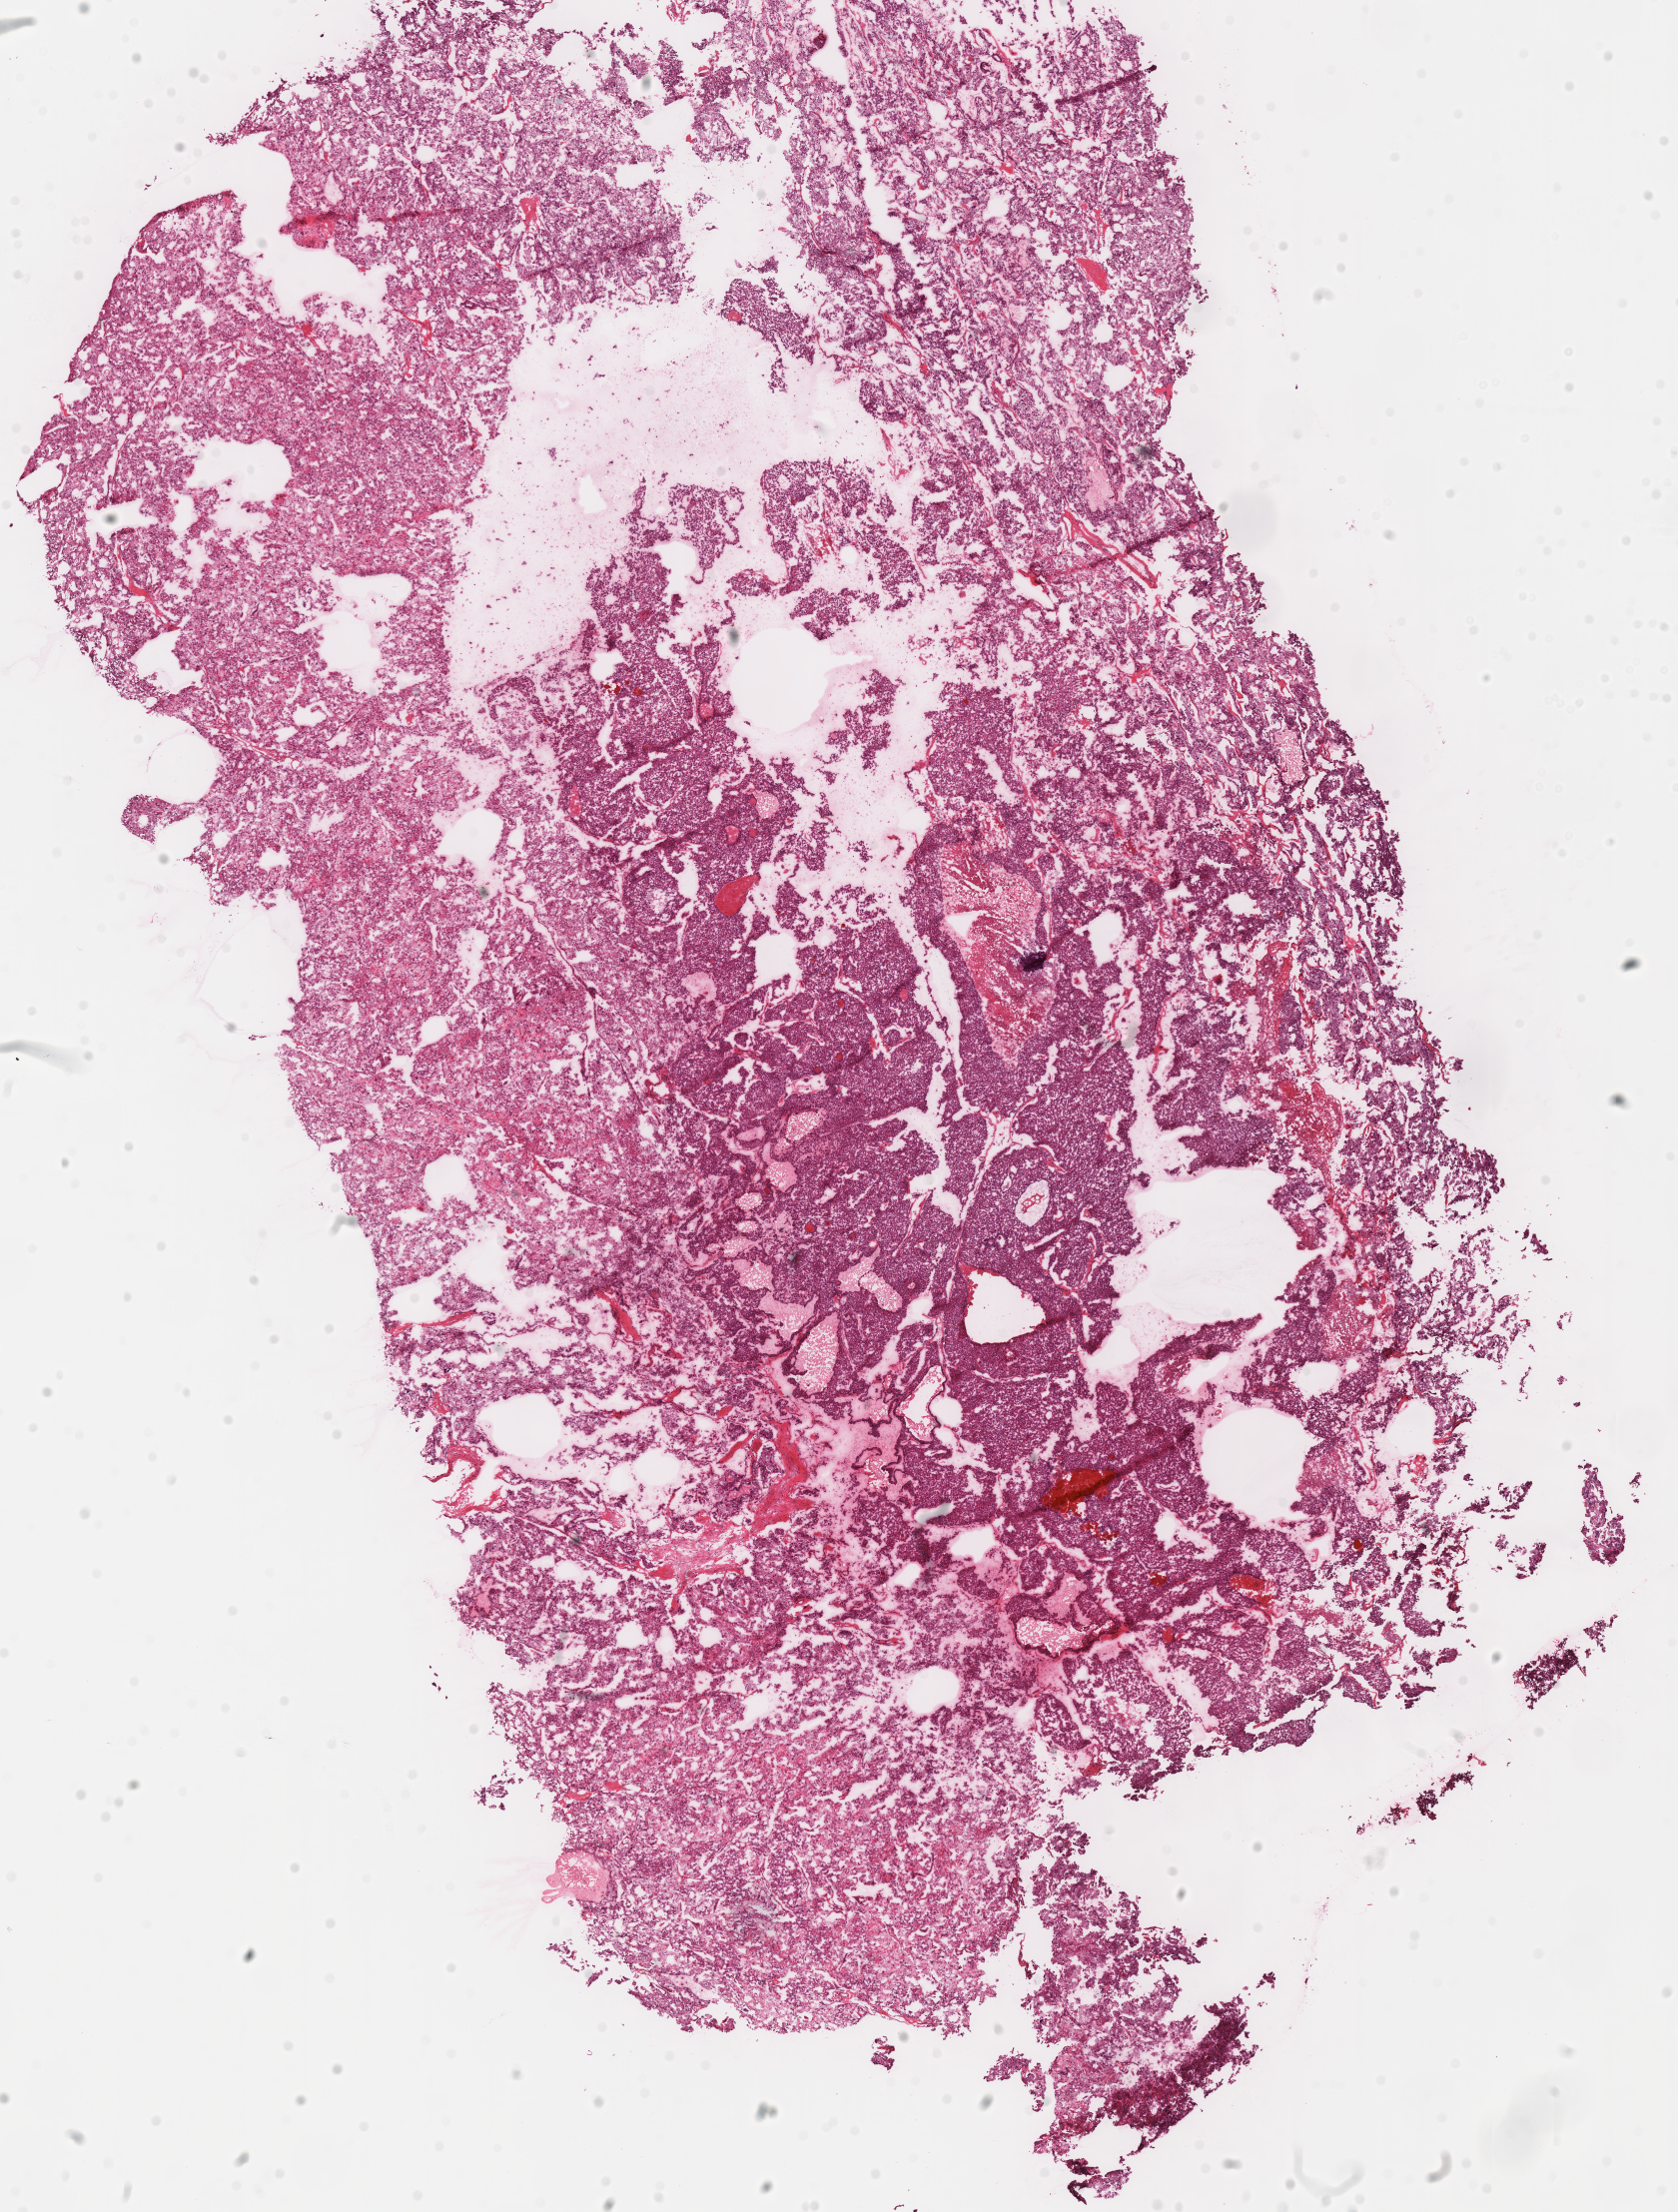
Whole-slide histology image, Hematoxylin and eosin (H&E) stained — whole scanned area (about 13.2 x 17.4 mm) shown as a low-resolution overview. Frozen section. Primary tumour sample from the kidney. Female, age 48 years at initial diagnosis. Composition of this section per pathologist review: tumour cells 100%, tumour nuclei 90%, normal cells 0%, stromal cells 0%, necrosis 0%. Infiltration values recorded for this section: lymphocyte infiltration 2%.
Lymph nodes positive (case pathology): 0 of 15 examined. AJCC pathologic stage: II. Pathologic diagnosis: Renal cell carcinoma, chromophobe type. Laterality: right.